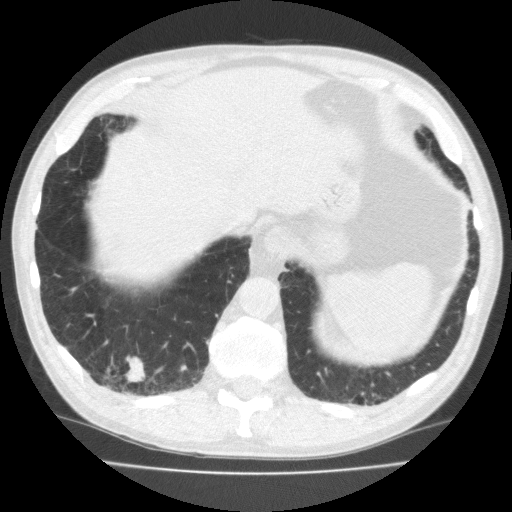
Low-dose screening chest CT, one axial slice; slice 49 of 195 in the series (ordered by position); reconstruction kernel FC10; lung window (W 1500 / L -600 HU); 512 × 512 image matrix, field of view 350 × 350 mm.
Annotated regions visible in this slice (outlined manually by an expert reader):
- lesion 1 (tumor, lower lobe of right lung): box from (x=125, y=356) to (x=146, y=382) px